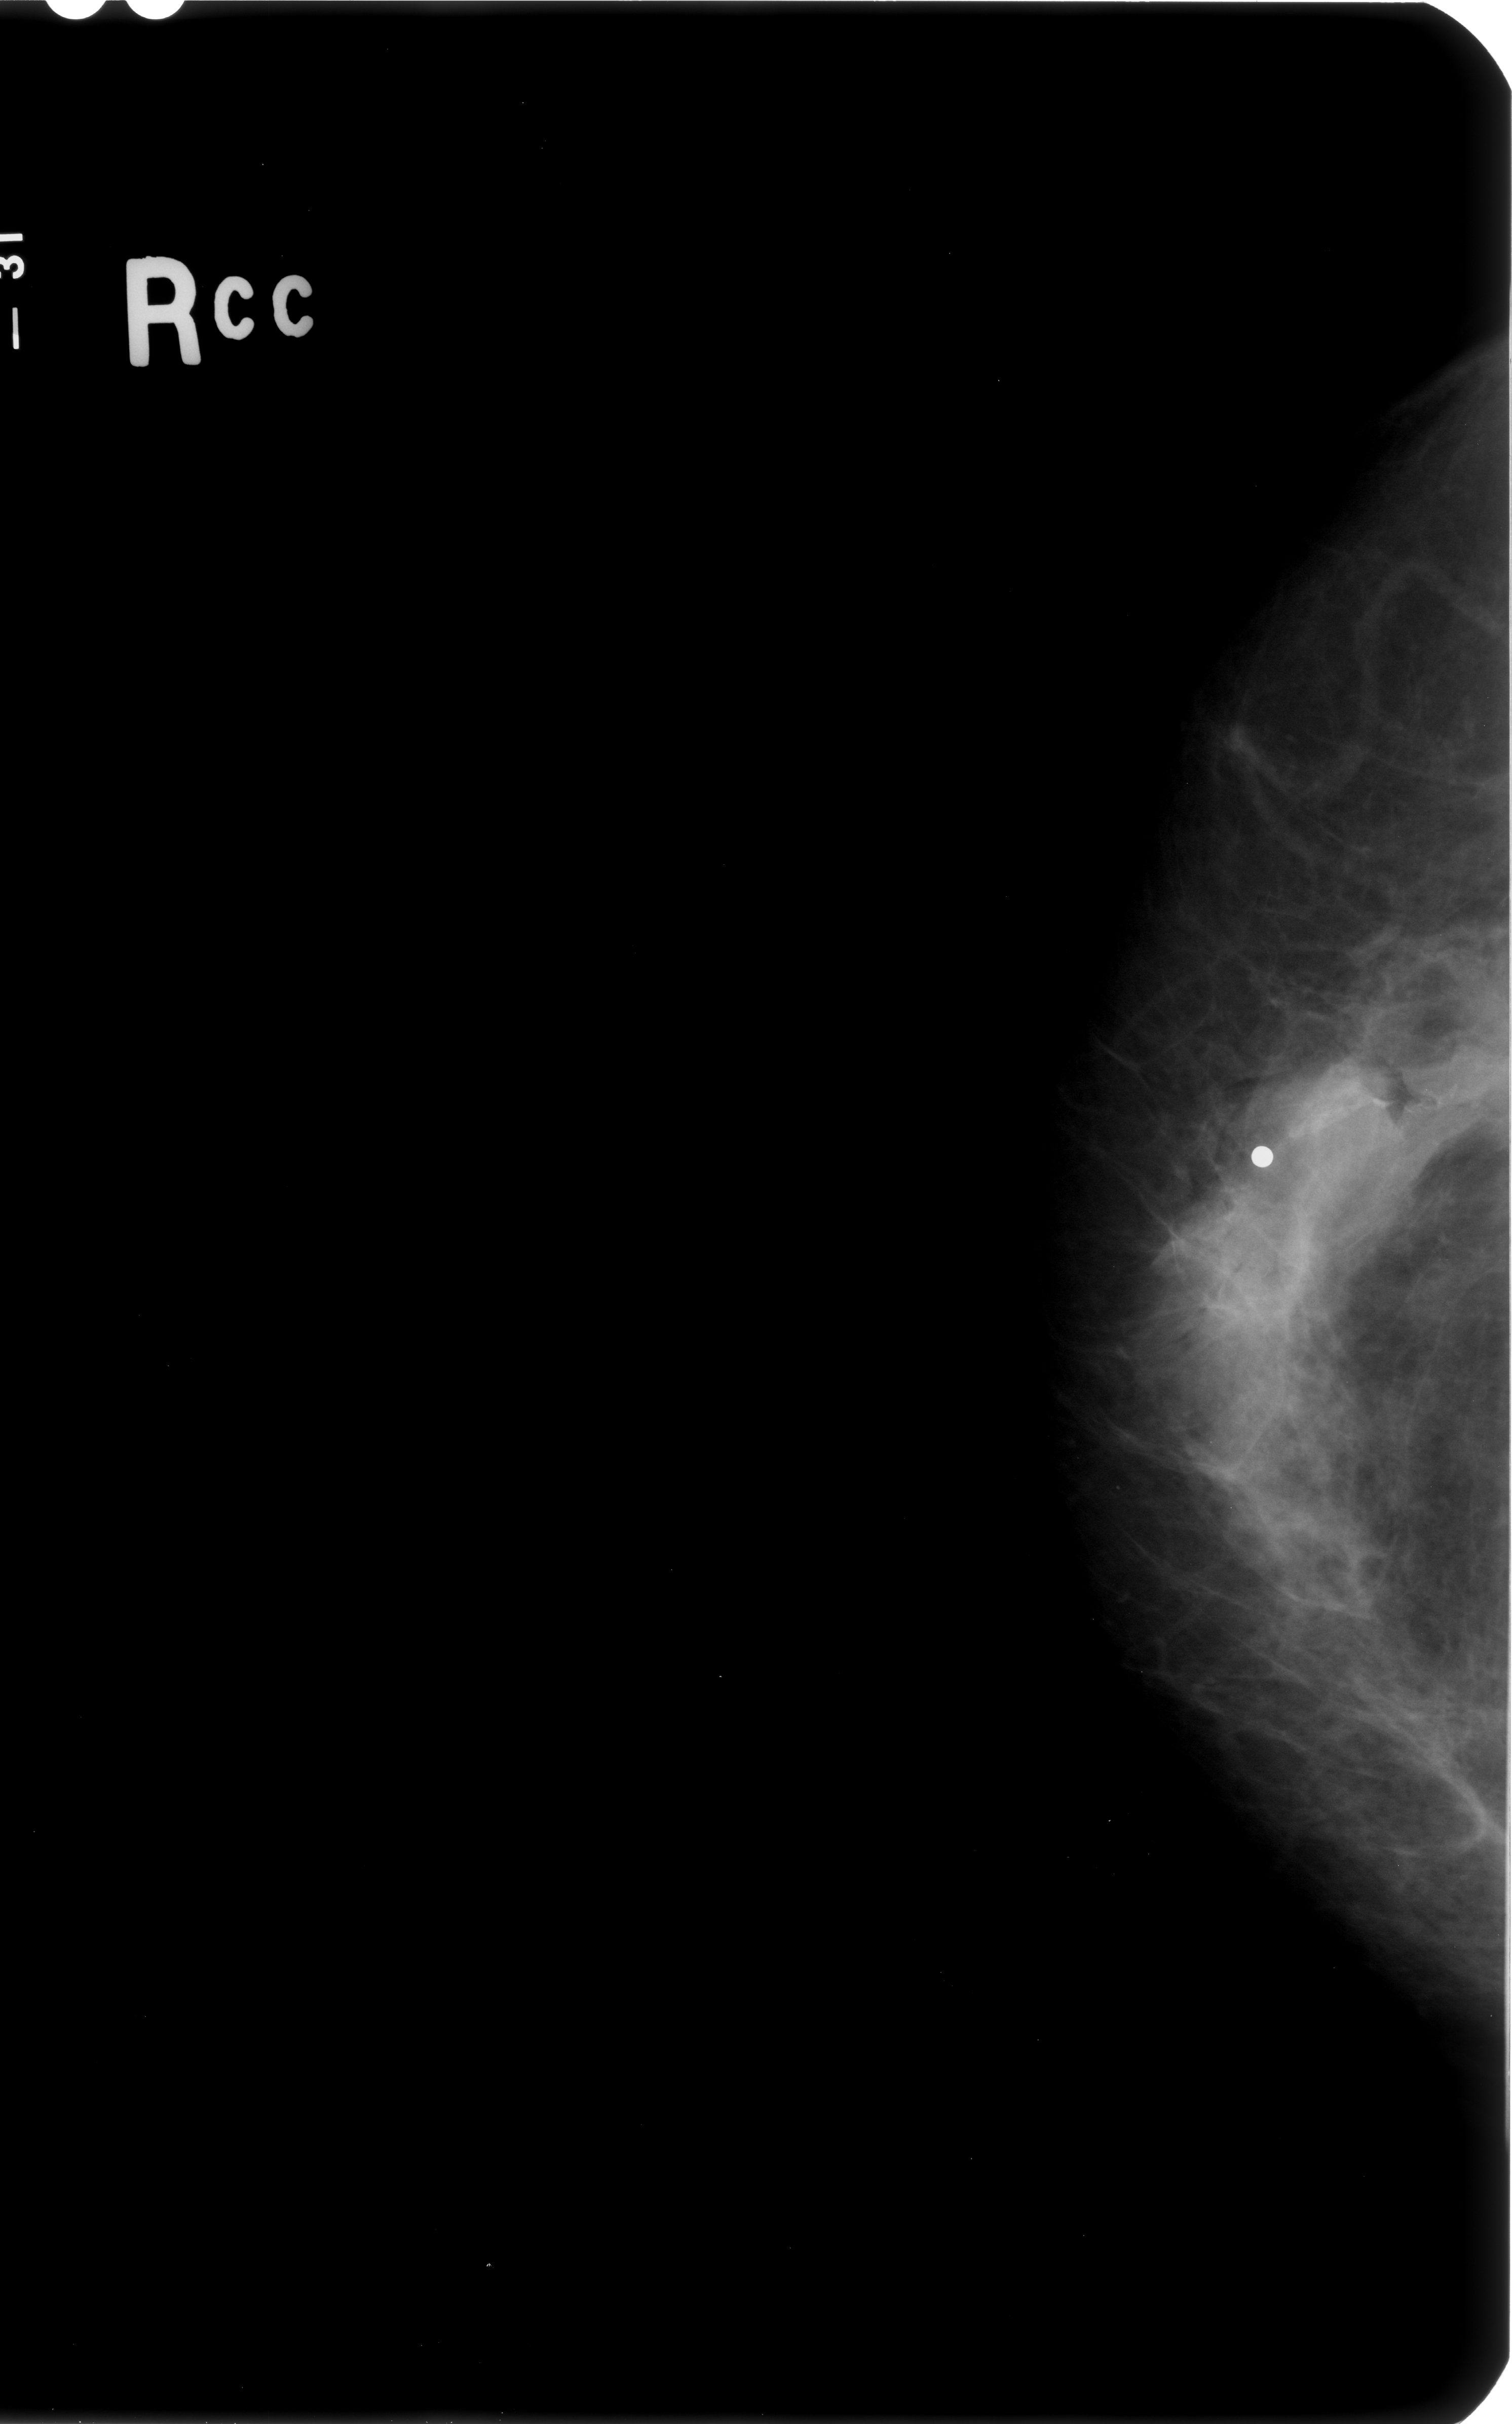
Digitized screen-film mammogram; right breast; CC view.
Calcifications, morphology fine linear branching, distribution linear; BI-RADS assessment category 4; subtlety rating 5 on a 1 (subtle) to 5 (obvious) scale; pathology result (as recorded, not read from the image): malignant.